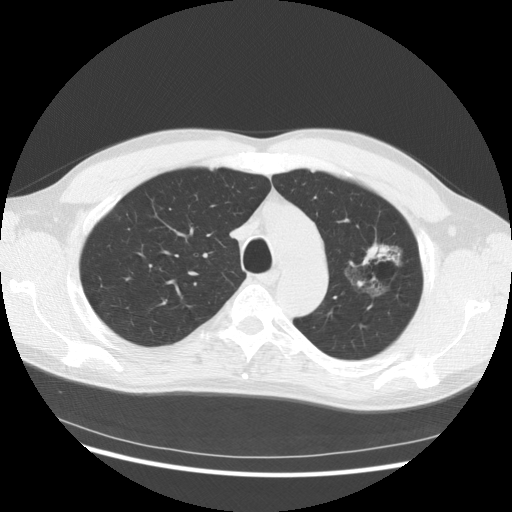
Chest CT (low-dose screening protocol), one axial image, third screening round (two years after baseline), lung window (W 1500 / L -600 HU), 2.5 mm slice thickness. Male, age 61 years at enrolment. Former smoker at enrolment.
Expert reader's lesion annotation, bounding box <332,234,409,314> (left, top, right, bottom; pixels). The exam's reader record, not a measurement of the box and not confirmed to be the same lesion: non-calcified nodule or mass ≥4 mm, left upper lobe, 37 × 33 mm, poorly defined margins, mixed attenuation, pre-existing on the prior screen: yes; interval growth: yes. Later outcome: lung cancer diagnosed 361 days after this screen — bronchiolo-alveolar adenocarcinoma, NOS, left upper lobe, well differentiated (G1), stage IB (AJCC 6th edition), 44 mm at pathology.